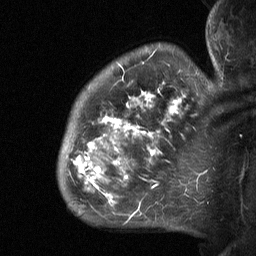
Breast MRI (dynamic contrast-enhanced), one sagittal slice; position 49 of 64 along the scan axis; dynamic contrast-enhanced study with each time point stored as its own series, time point 2 of 3 at this slice position (early post-contrast, ordered by acquisition time); 1.5 T; TE 4.8 ms, TR 27 ms; 2.3 mm slice thickness; 256 × 256 image matrix. Female patient, age 50 years. From the clinical record (not read from this slice): setting: breast cancer imaged before/during neoadjuvant chemotherapy; receptor status: HER2-positive.
Annotated regions visible in this slice (semi-automatically segmented with operator editing):
- analysis volume of interest (the breast-tissue region the enhancement analysis was run in; not a lesion): box from (x=57, y=64) to (x=211, y=218) px
- tumour enhancement mask (voxels above the 90 % enhancement threshold inside the analysis volume of interest): (x=73, y=78)–(x=185, y=206)